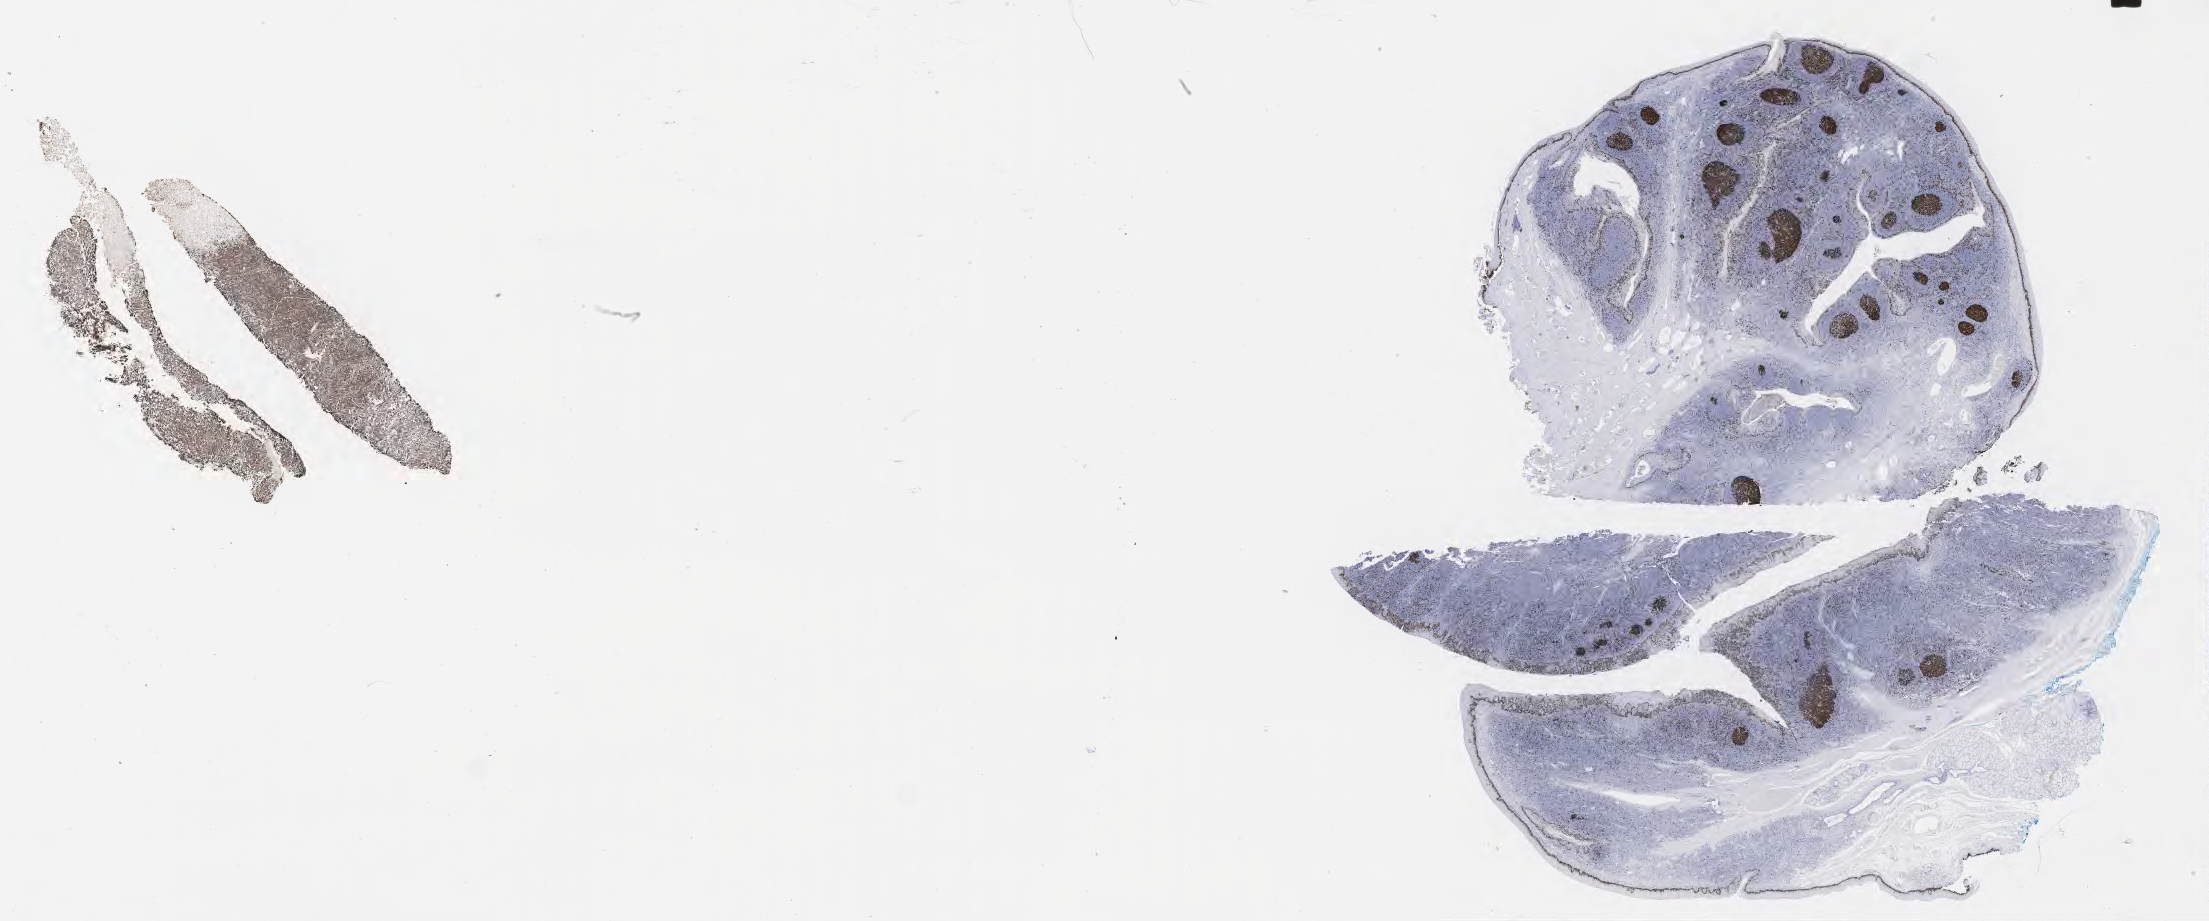
Immunohistochemistry (IHC) whole-slide image stained for Ki-67, a low-resolution overview of the entire scanned area, about 35.7 x 14.9 mm; specimen: tumor tissue. Female patient, aged 18.
Diagnosis: Burkitt lymphoma, NOS.